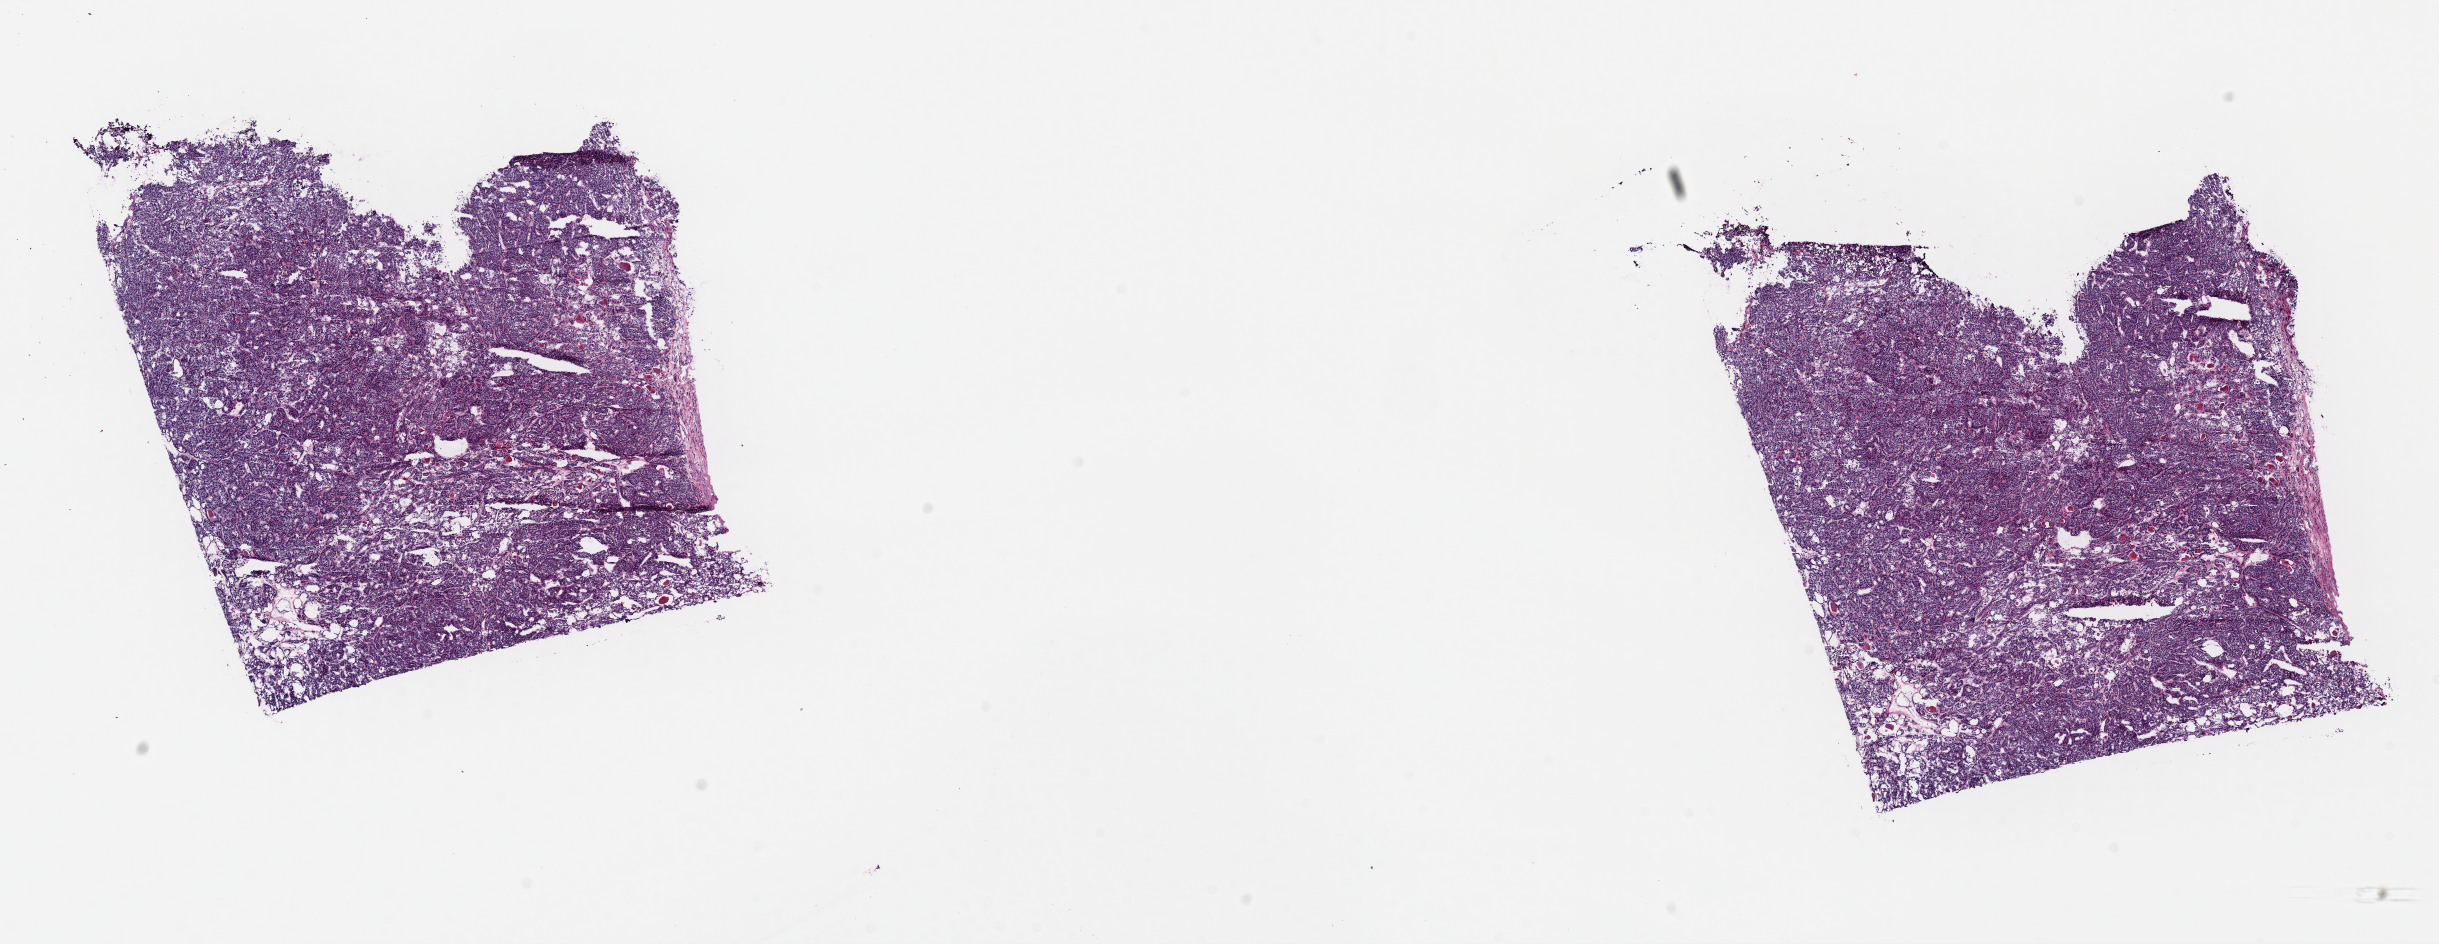
Hematoxylin and eosin (H&E) stained whole-slide image, a low-resolution overview of the entire scanned area, about 19.3 x 7.5 mm (from a 40x scan). Frozen section from the top of the tissue portion. Sample: primary tumour, thyroid. Male patient; age at initial diagnosis 79 years. Composition of this section per pathologist review: tumour cells 90%, tumour nuclei 90%, normal cells 0%, stromal cells 10%, necrosis 0%. Infiltration values recorded for this section: lymphocyte infiltration 2%, monocyte infiltration 0%, neutrophil infiltration 0%.
- AJCC pathologic stage: II (7th edition)
- TNM: T2 N0 M0
- laterality: left
- diagnosis: Papillary adenocarcinoma, NOS (thyroid gland)